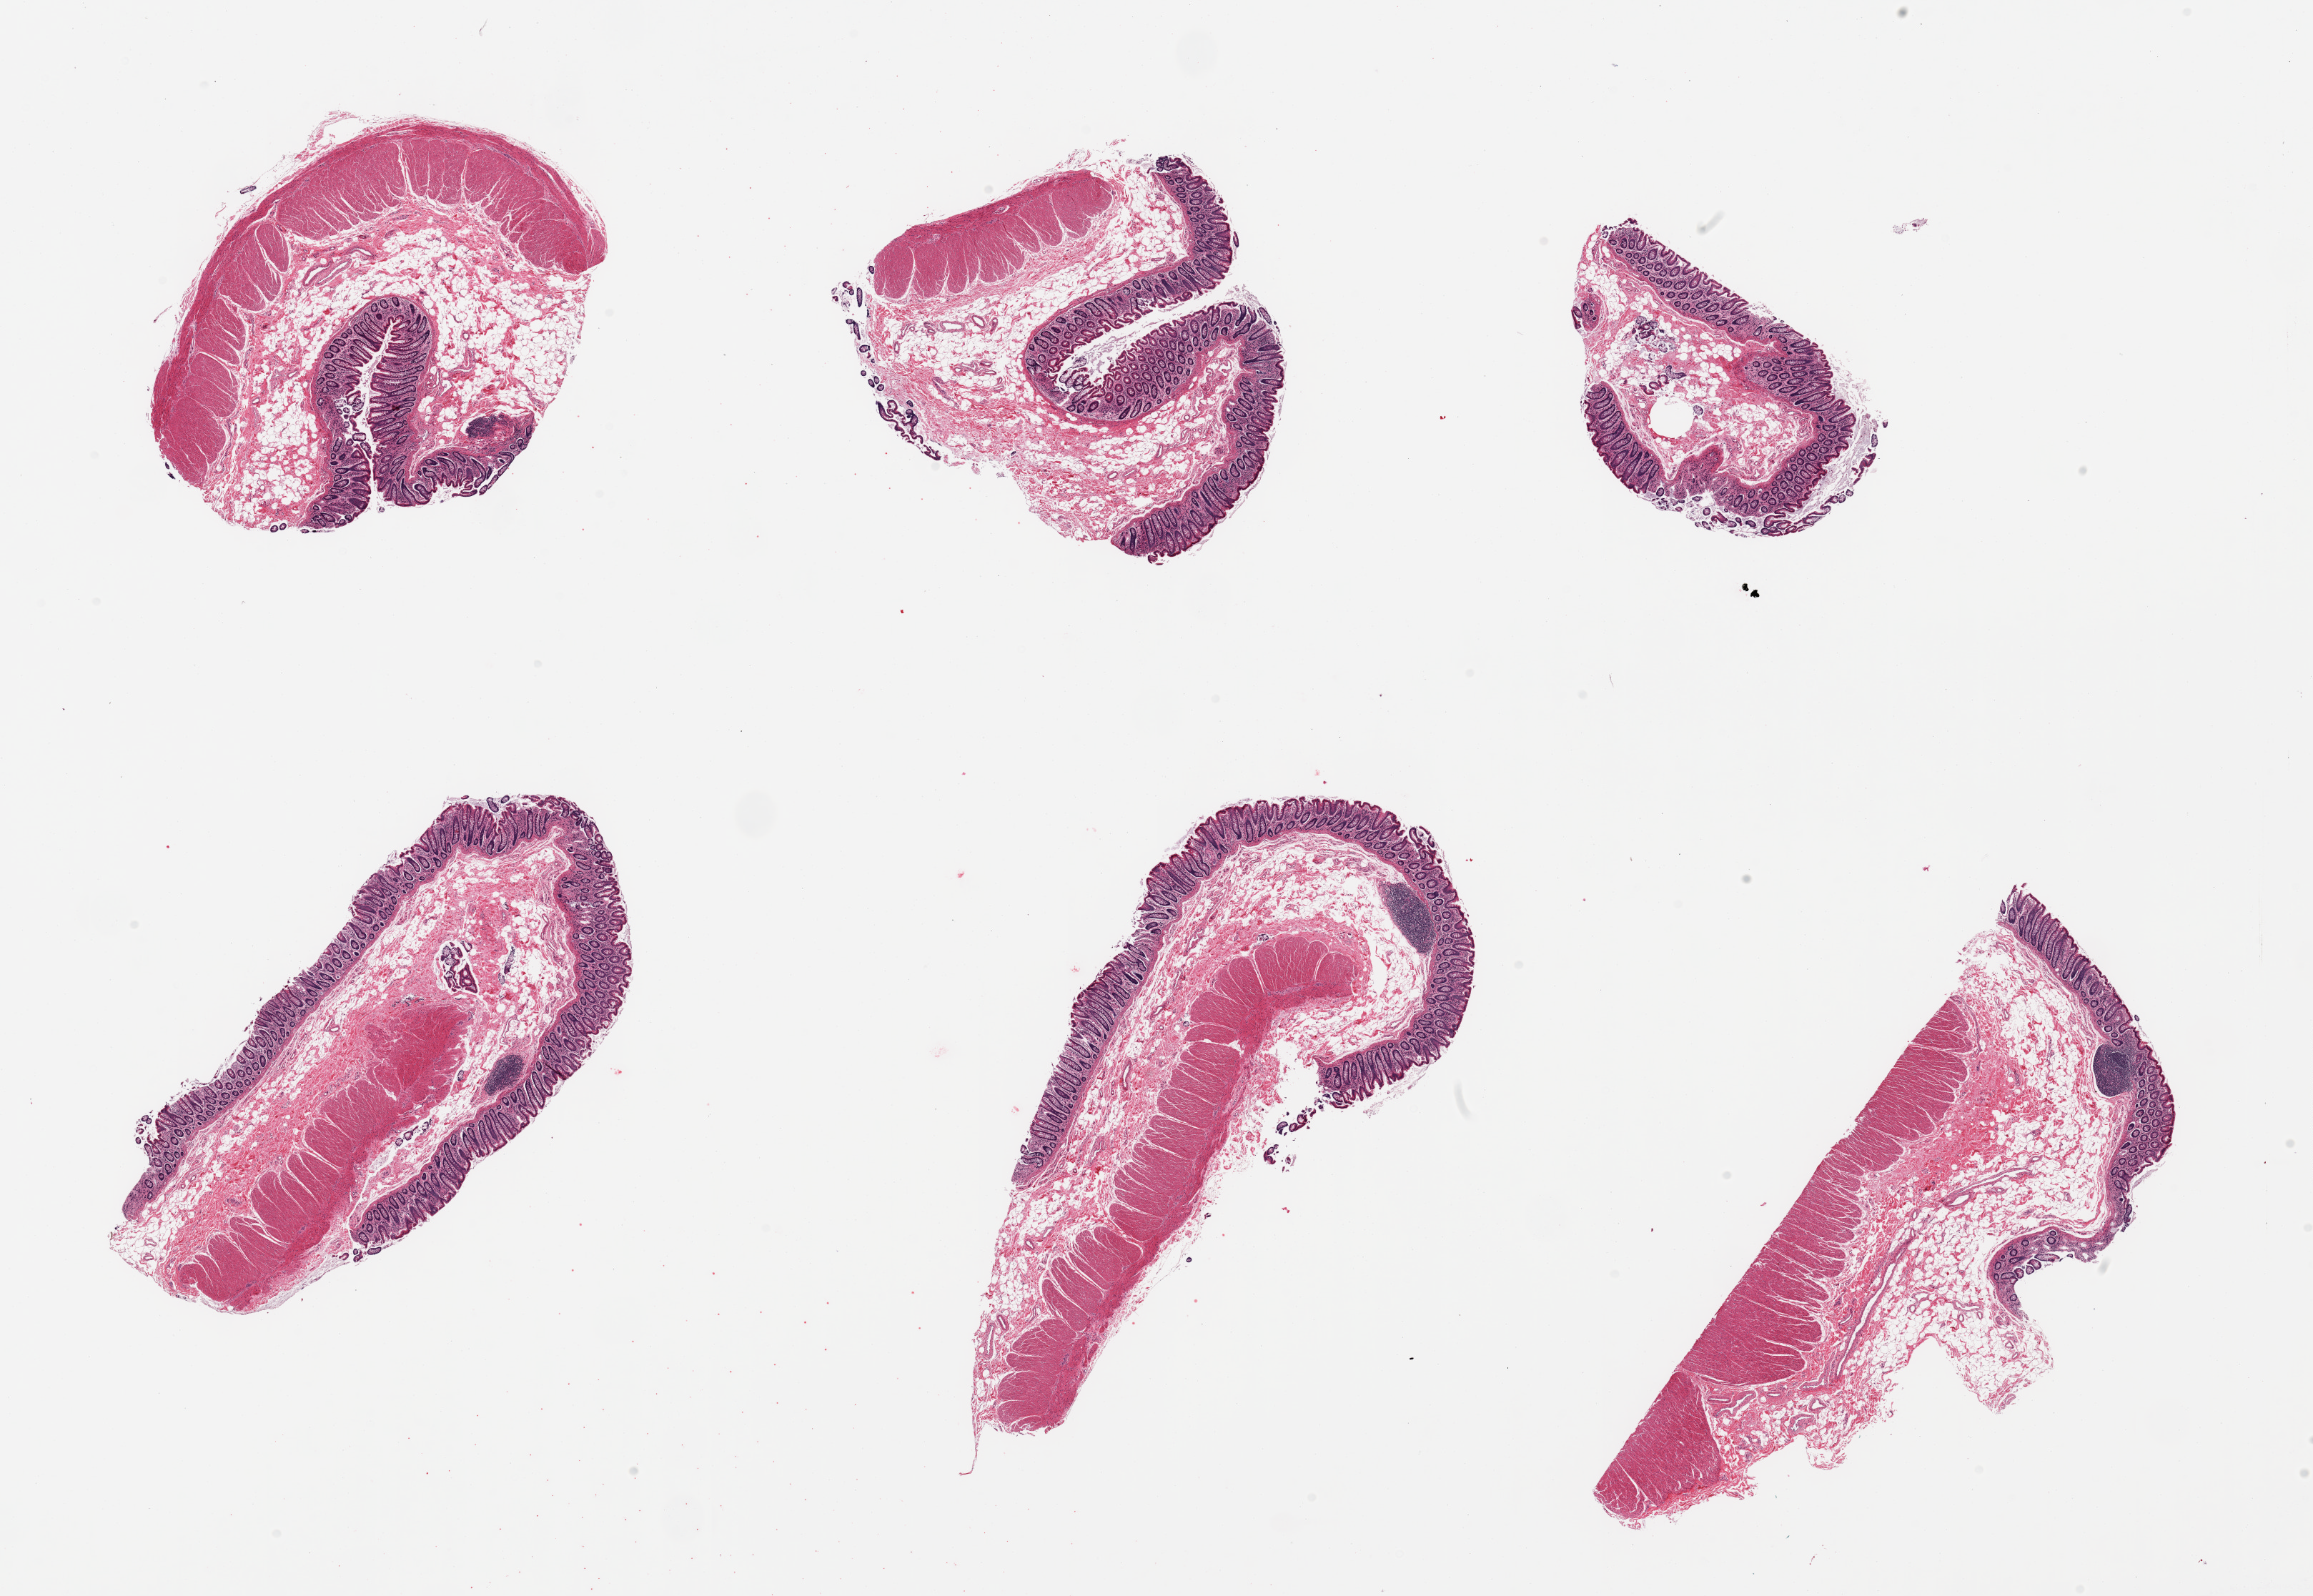
Hematoxylin and eosin (H&E) whole-slide image, brightfield — shown as a low-resolution overview of the whole scanned area (about 25.6 x 17.7 mm, slide scanned at 20x); PAXgene-fixed, paraffin-embedded tissue; target tissue: transverse colon; tissue donor sample. Donor: female.
- review note (as recorded): 6 pieces; 1 without muscularis propria